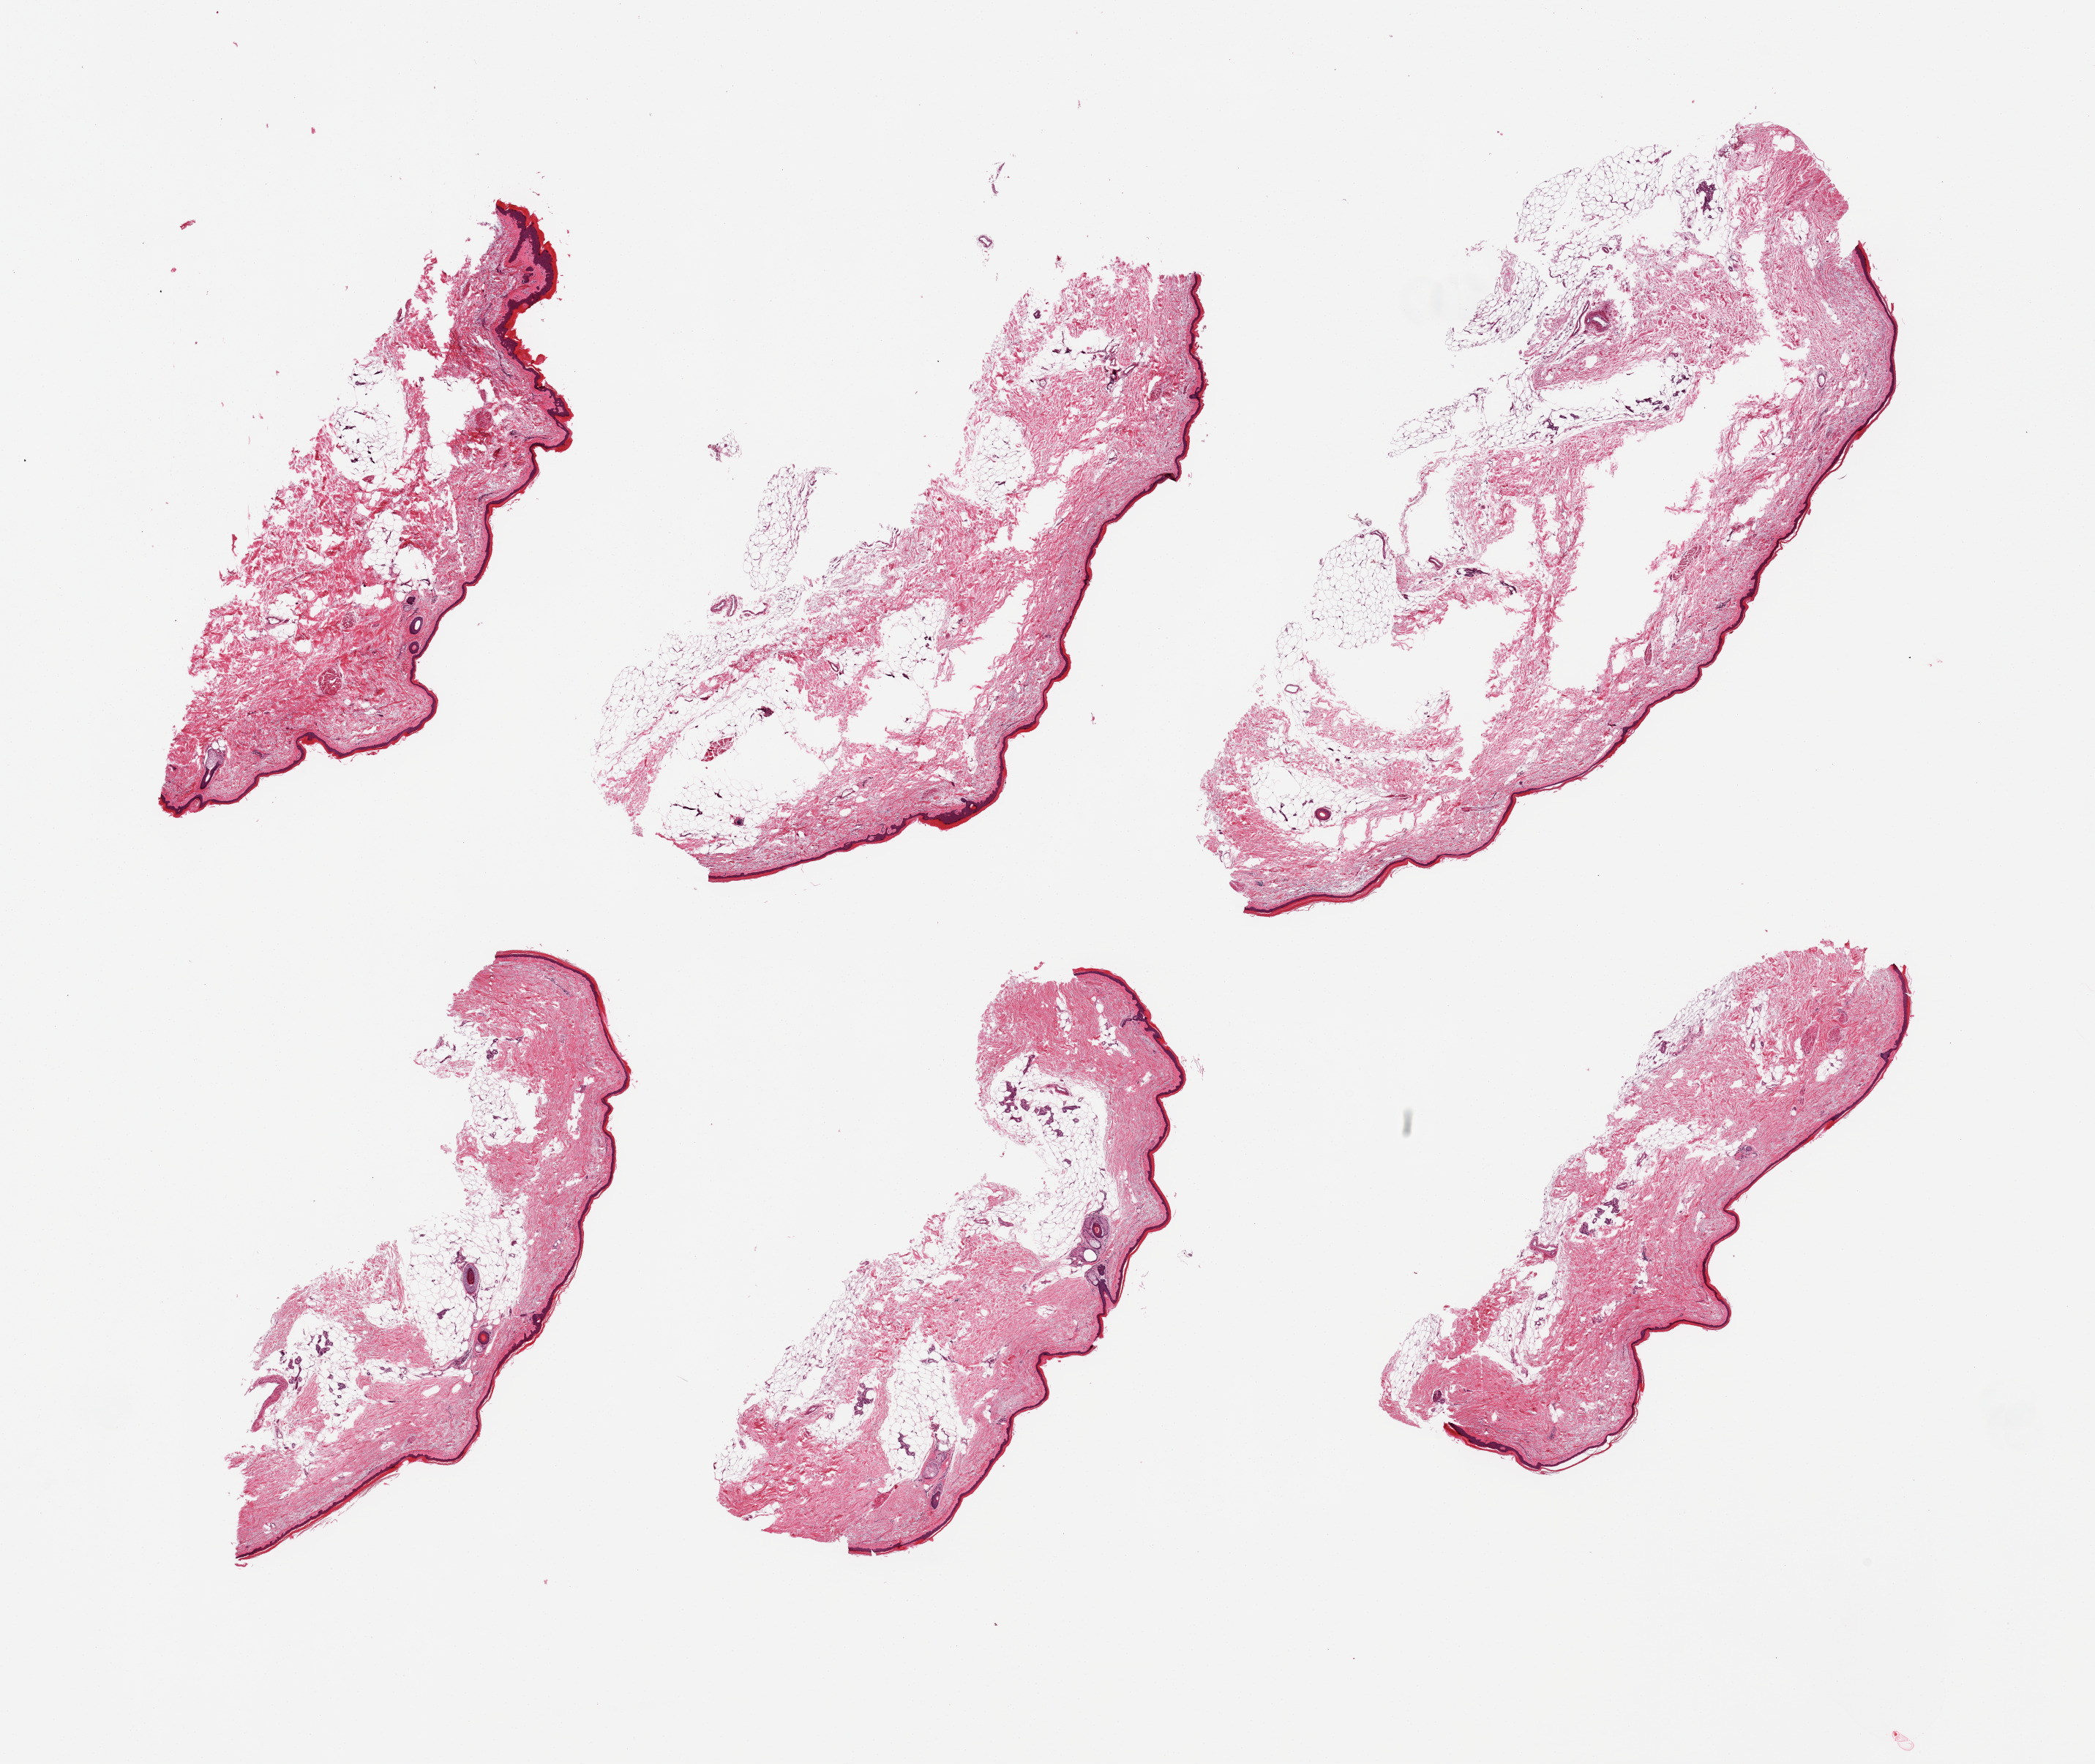
Hematoxylin and eosin (H&E) whole-slide image, whole scanned area (about 22.6 x 19.1 mm) shown as a low-resolution overview, PAXgene-fixed, paraffin-embedded tissue, section of skin of lower leg (target tissue), donor tissue sample. Female donor.
Reviewer comment on this tissue sample: 6 pieces; dermal elastosis; 50% dermal fat.